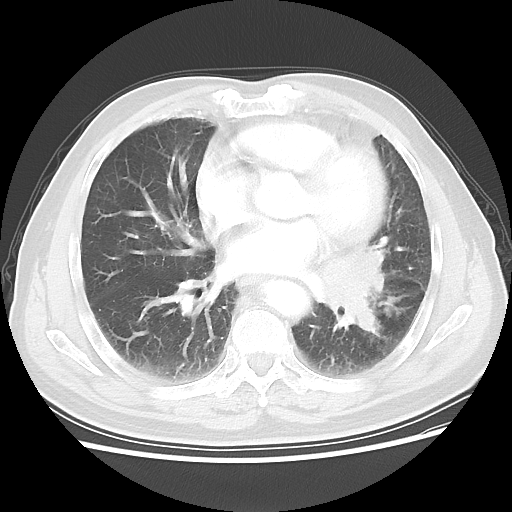
Chest CT, one axial slice; slice 27 of 56 in the series (ordered by position); reconstruction kernel LUNG; 120 kVp; lung window (W 1500 / L -600 HU); 5 mm slice thickness; 512 × 512 image matrix. Male patient, age 75 years. From the clinical record (not read from this slice): clinical TNM (as recorded): T3 N0 M0.
Structures marked on this image (bounding box drawn by a radiologist):
- lung tumour (recorded histology: squamous cell carcinoma): bounding box <313,236,404,338> (left, top, right, bottom; pixels)